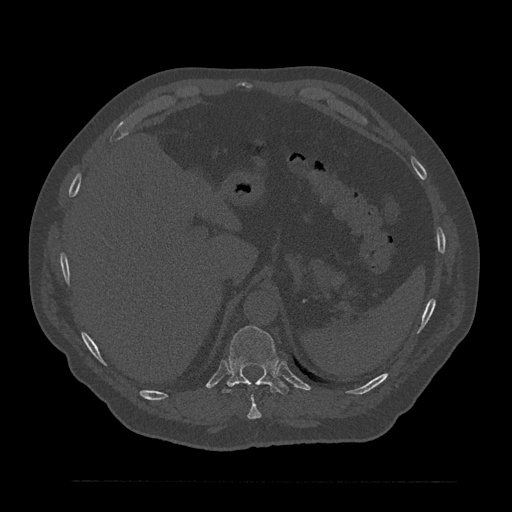
CT including the spine, one axial slice. Slice 311 of 797 in the series (ordered by position). Reconstruction kernel Br40s/3. 120 kVp. Bone window (W 1800 / L 400 HU). 0.5 mm slice thickness. 512 × 512 image matrix, field of view 430 × 430 mm. Male patient, age 61 years. Case-level facts recorded for this patient, not image findings: primary cancer: prostate.
Structures marked on this image (semi-automatic segmentation, software-assisted and operator-edited):
- T10 vertebra: bounding box <247,394,262,420> (left, top, right, bottom; pixels)
- T11 vertebra: <222,326,289,395>